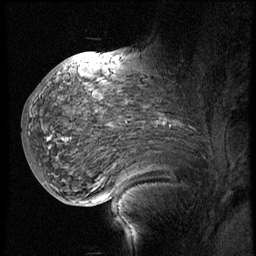
Breast MRI (dynamic contrast-enhanced), one sagittal slice. Slice 34 of 60 in the series (ordered by position). 3 images stored at this slice position (order not interpretable as contrast timing). 1.5 T. TE 4.2 ms, TR 8.9 ms. 2.5 mm slice thickness. 256 × 256 image matrix, field of view 200 × 200 mm. Female patient, age 57 years. From the clinical record (not read from this slice): setting: breast cancer imaged before/during neoadjuvant chemotherapy; receptor status: HER2-positive.
Structures marked on this image (semi-automatic segmentation, software-assisted and operator-edited):
- analysis volume of interest (the breast-tissue region the enhancement analysis was run in; not a lesion): bounding box <34,75,214,171> (left, top, right, bottom; pixels)
- tumour enhancement mask (voxels above the 140 % enhancement threshold inside the analysis volume of interest): <67,121,160,140>